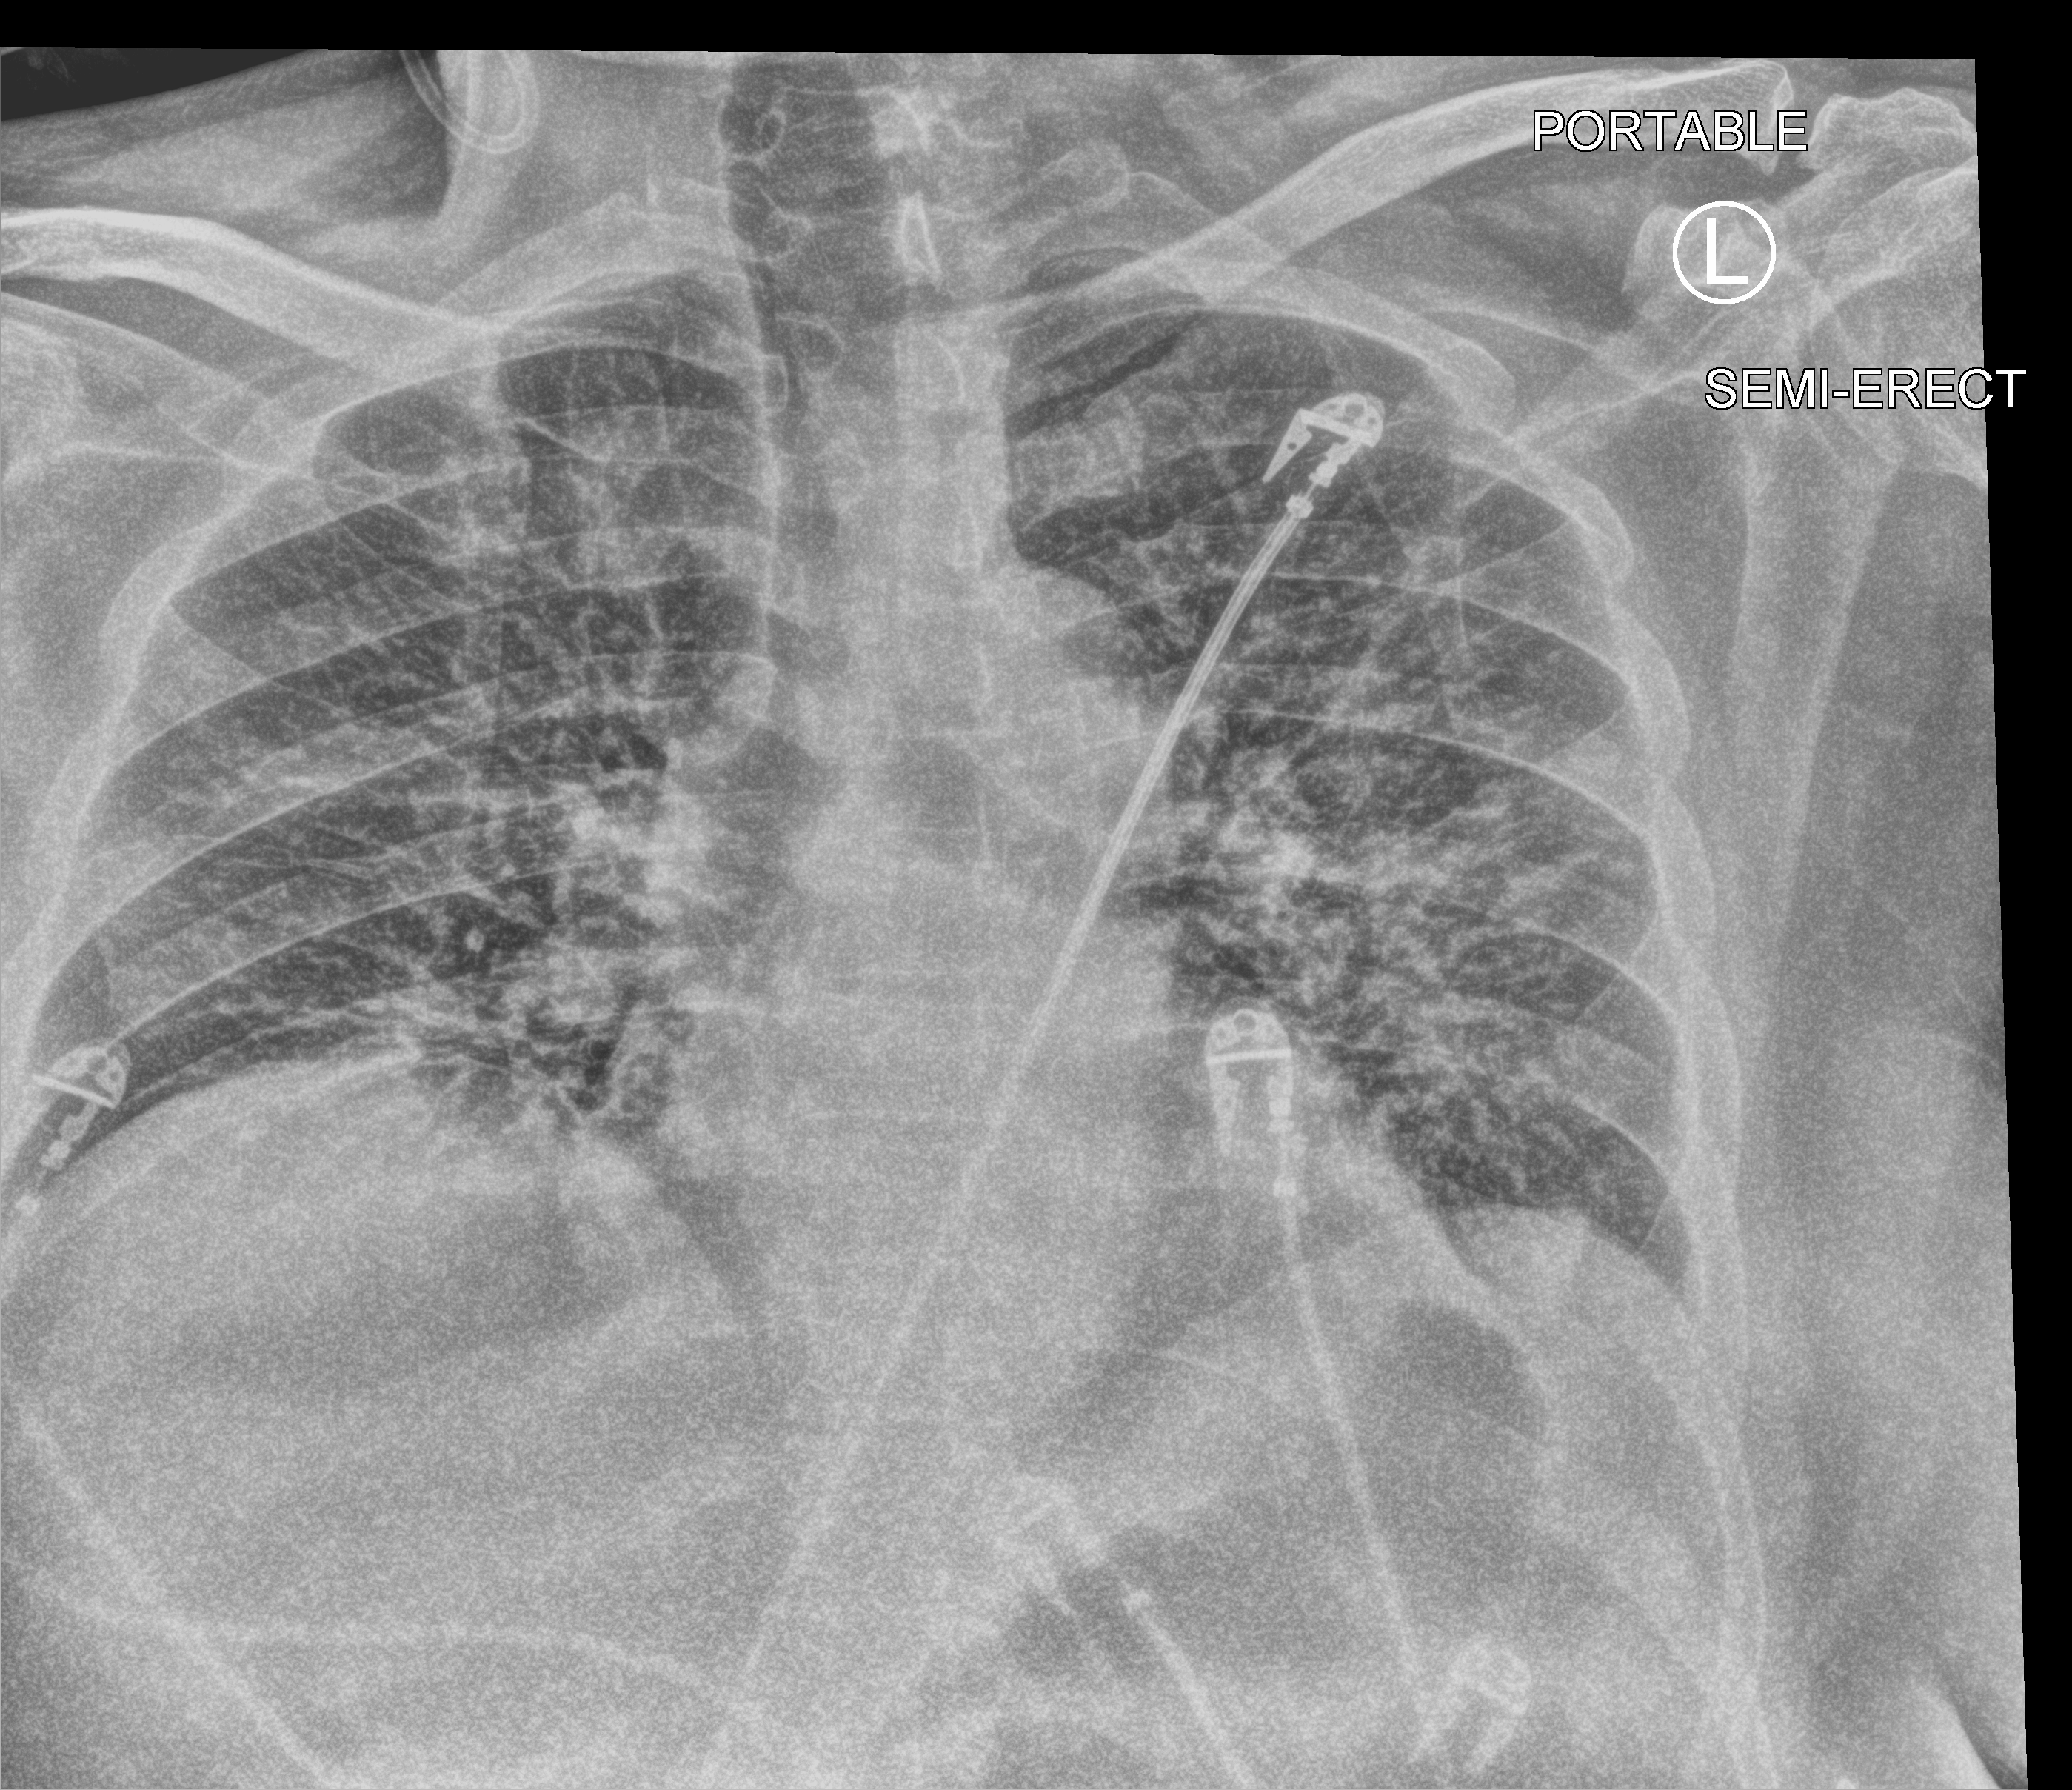
Chest X-ray (portable), anteroposterior (AP) projection. Patient hospitalised with COVID-19; male, aged 18–59 years.
Hospital-stay facts (about this admission, not read from this image; timing relative to this image not recorded): length of hospital stay: 7 days.